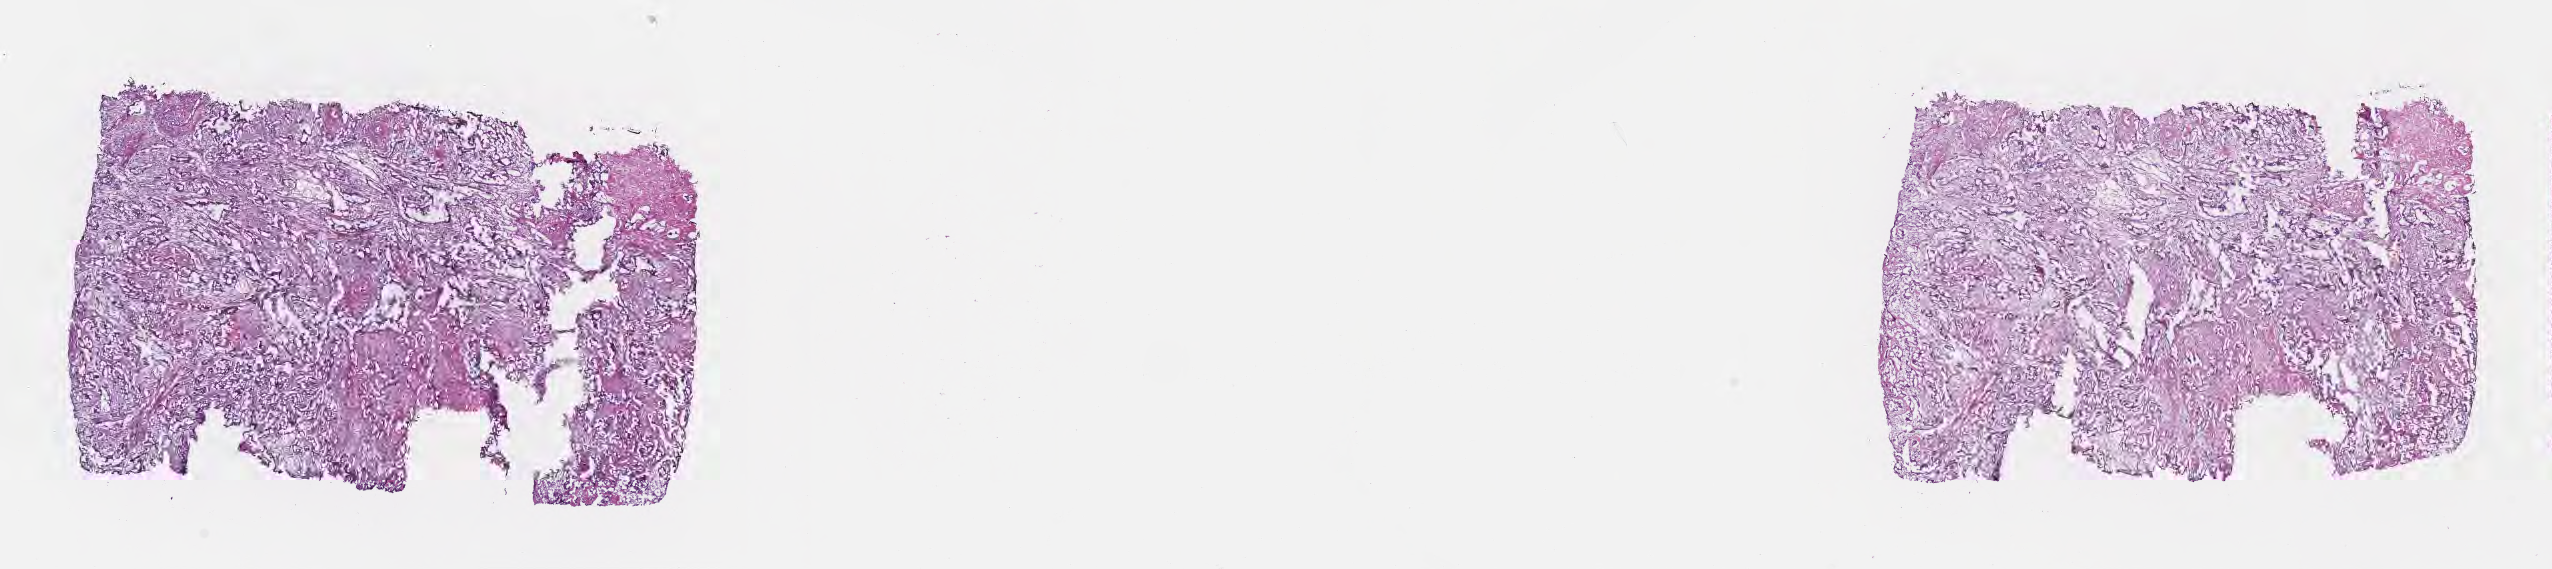
Digitized H&E-stained section, shown as a low-resolution overview of the whole scanned area (about 20.6 x 4.6 mm). Cryosection. Primary tumor. Anatomic site: extrahepatic bile duct. Female patient; age at initial diagnosis 75 years. Slide review estimates, as recorded: tumor cells 80%, tumor nuclei 80%, stromal cells 20%, necrosis 0%, normal cells 0%. Infiltration values recorded for this section: lymphocyte infiltration 5%, monocyte infiltration 2%, neutrophil infiltration 7%.
Histologic diagnosis: Cholangiocarcinoma. Section: bottom of the tissue portion. AJCC pathologic stage: Stage IIIB.